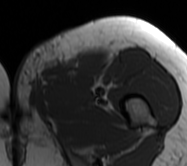
MRI of an extremity soft-tissue mass, one axial slice; position 17 of 62 along the scan axis; MR volume resampled by the dataset authors to the PET/CT grid (not the native acquisition matrix); 3.27 mm slice thickness; 187 × 166 image matrix, field of view 183 × 162 mm. Female patient. From the clinical record (not read from this slice): histological type: leiomyosarcoma; grade: high; site of the primary tumour: groin.
Outlined on this slice (expert contour drawn on MRI and transferred to this co-registered scan by the dataset authors):
- gross tumour volume including surrounding oedema: box from (x=14, y=42) to (x=106, y=120) px
- gross tumour volume (mass): (x=43, y=51)–(x=104, y=89)